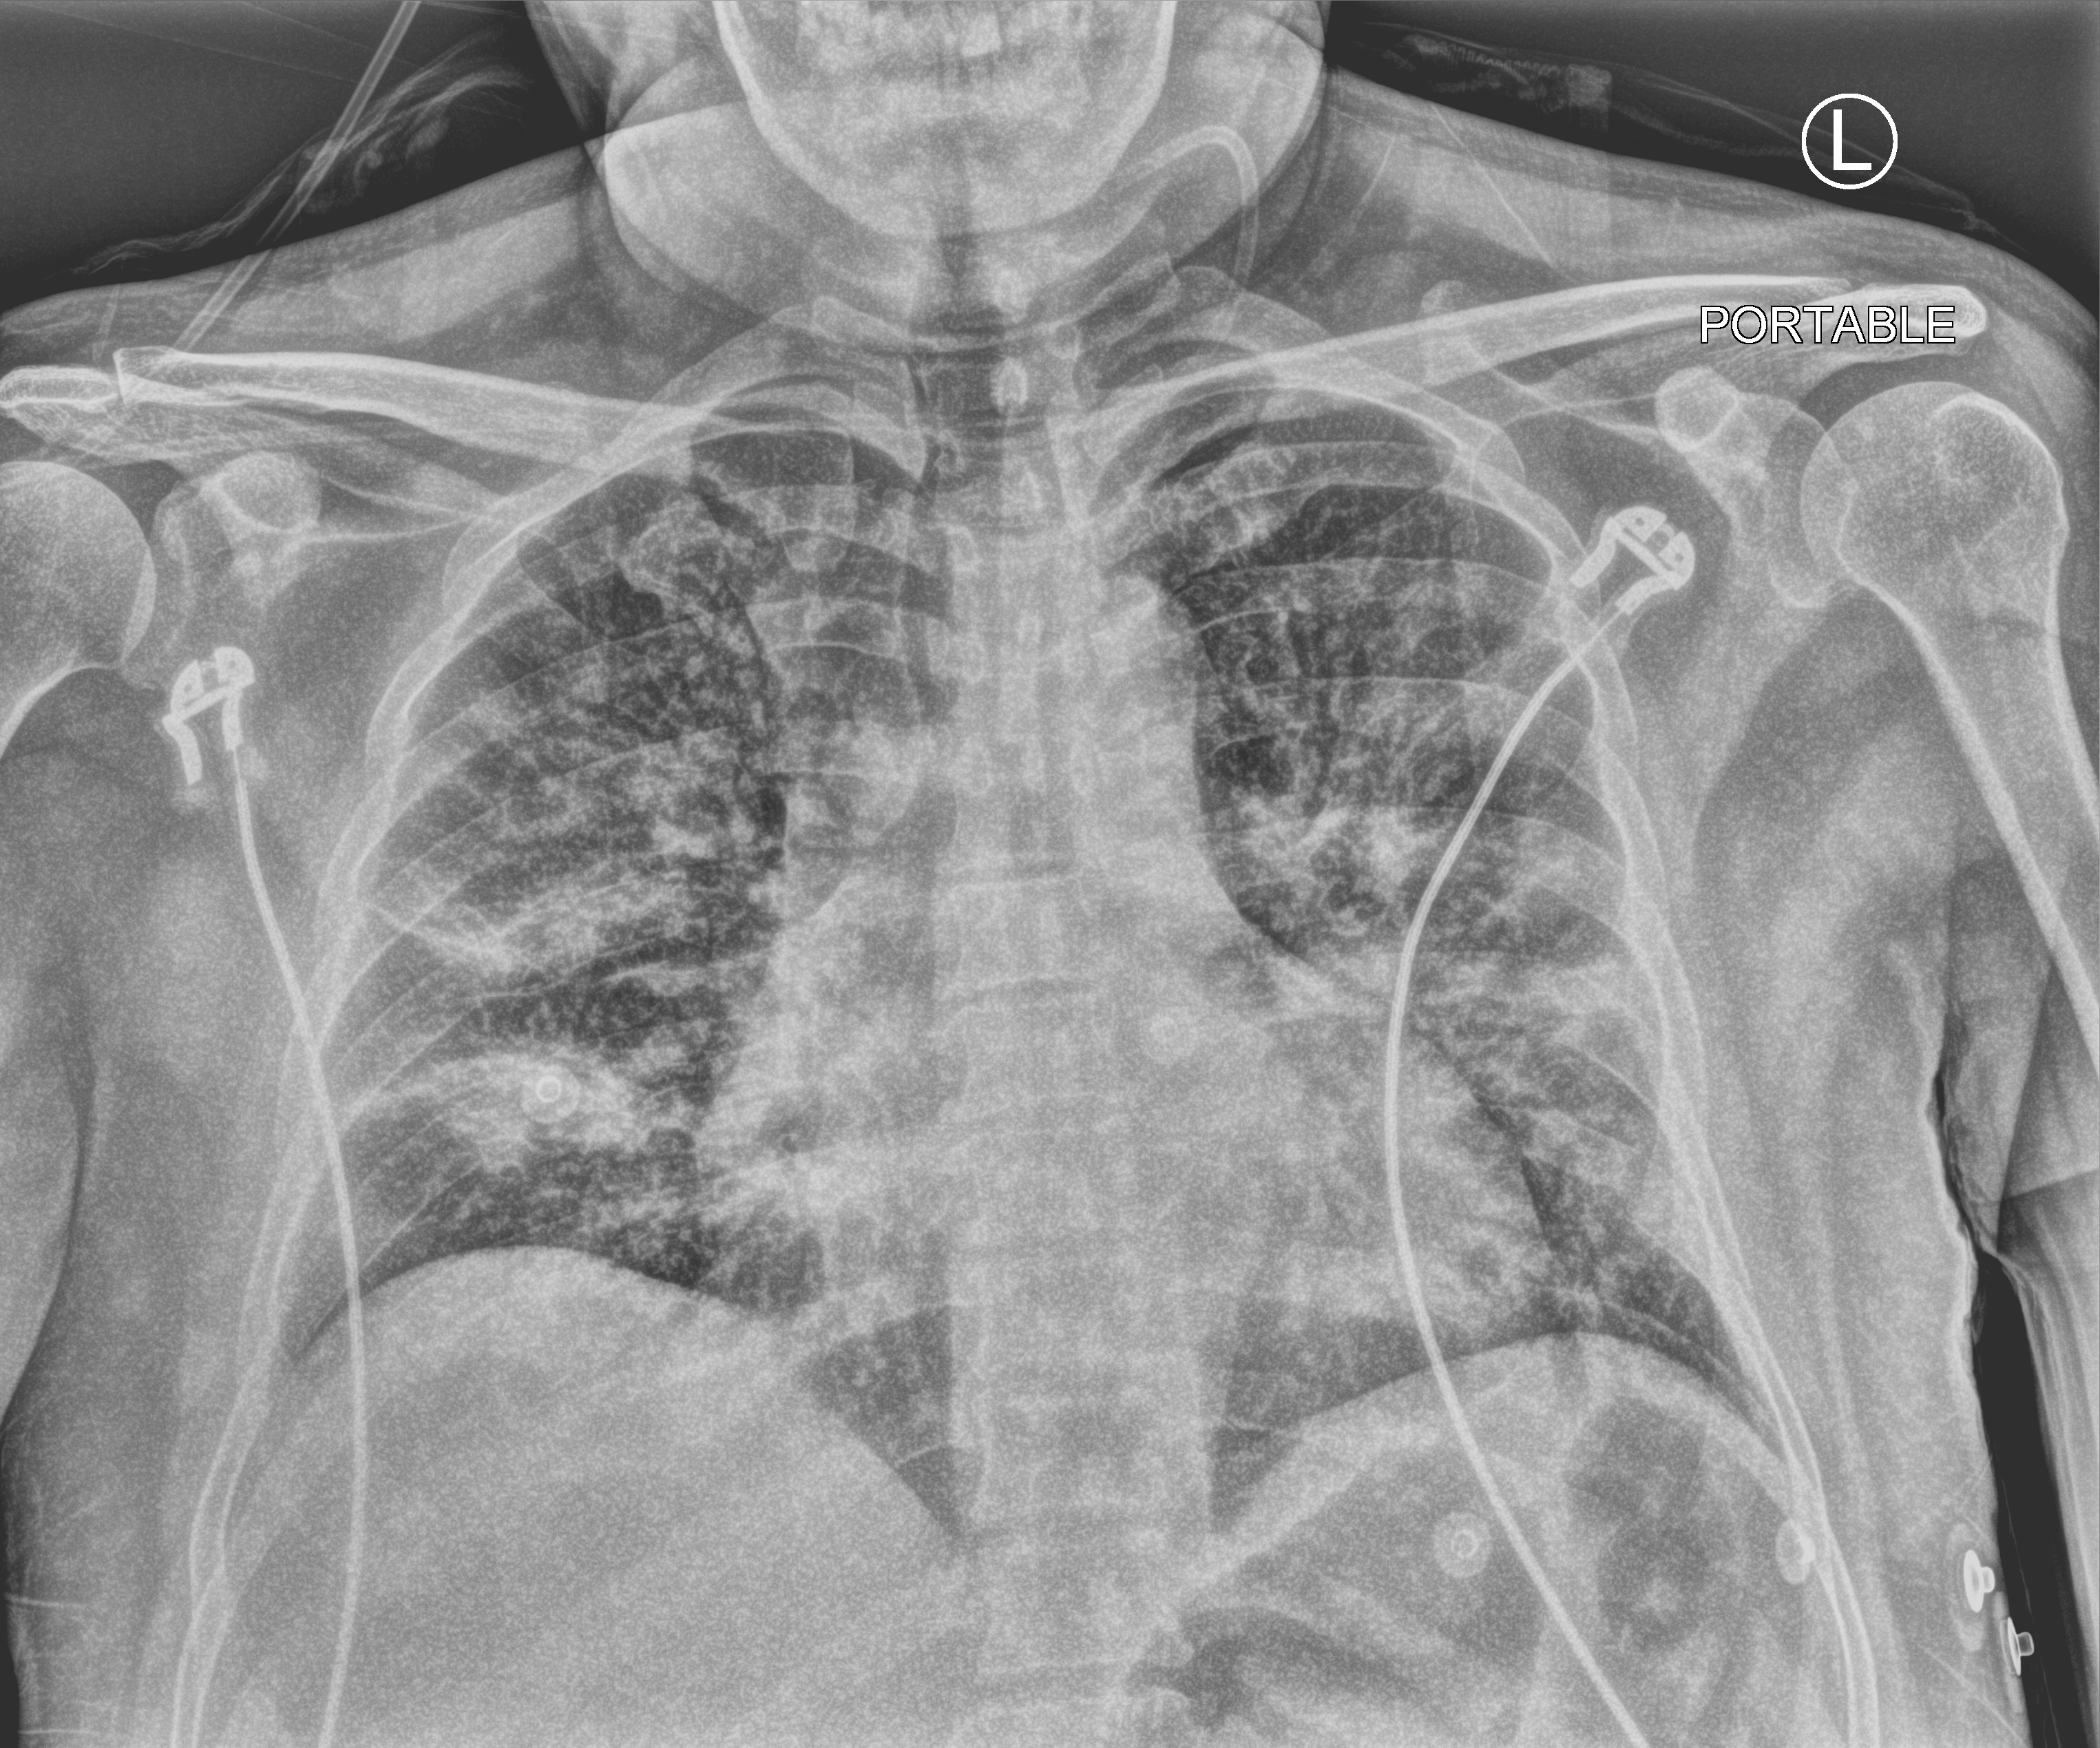
Portable chest radiograph, anteroposterior (AP) projection. Male patient hospitalised with COVID-19, age 18–59 years.
From the hospital-stay record, not from the radiograph (when in the stay this image was taken is not recorded):
- admitted to intensive care during this hospital stay: no